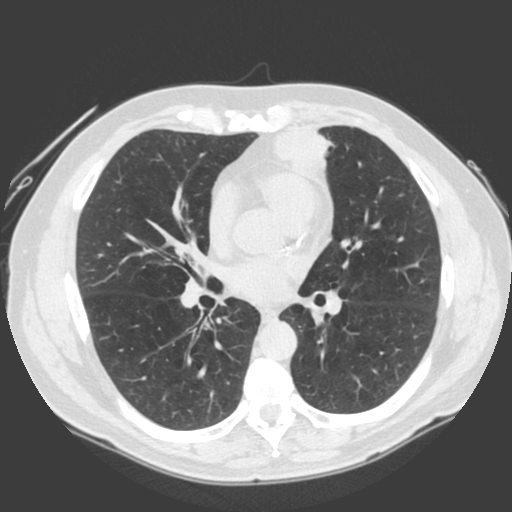
Low-dose screening chest CT, one axial slice. Slice 95 of 185 in the series (ordered by position). 120 kVp. Lung window (W 1500 / L -600 HU). 2 mm slice thickness. 512 × 512 image matrix, field of view 360 × 360 mm.
Structures marked on this image (manually delineated by an expert):
- lesion 1 (tumor, lower lobe of left lung): bounding box [x1, y1, x2, y2] px = [275, 125, 335, 174]